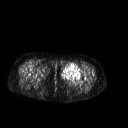
FDG PET of an extremity soft-tissue mass (from a PET/CT study), one axial slice. Slice 247 of 267 in the series (ordered by position). 3.27 mm slice thickness. 128 × 128 image matrix. Patient: female, 42 years. Case-level facts recorded for this patient, not image findings: histological type: pleiomorphic leiomyosarcoma; grade: intermediate; site of the primary tumour: left thigh.
Annotated regions visible in this slice (expert contour drawn on MRI and transferred to this co-registered scan by the dataset authors):
- gross tumour volume including surrounding oedema: box from (x=60, y=63) to (x=82, y=81) px
- gross tumour volume (mass): (x=60, y=63)–(x=82, y=81)